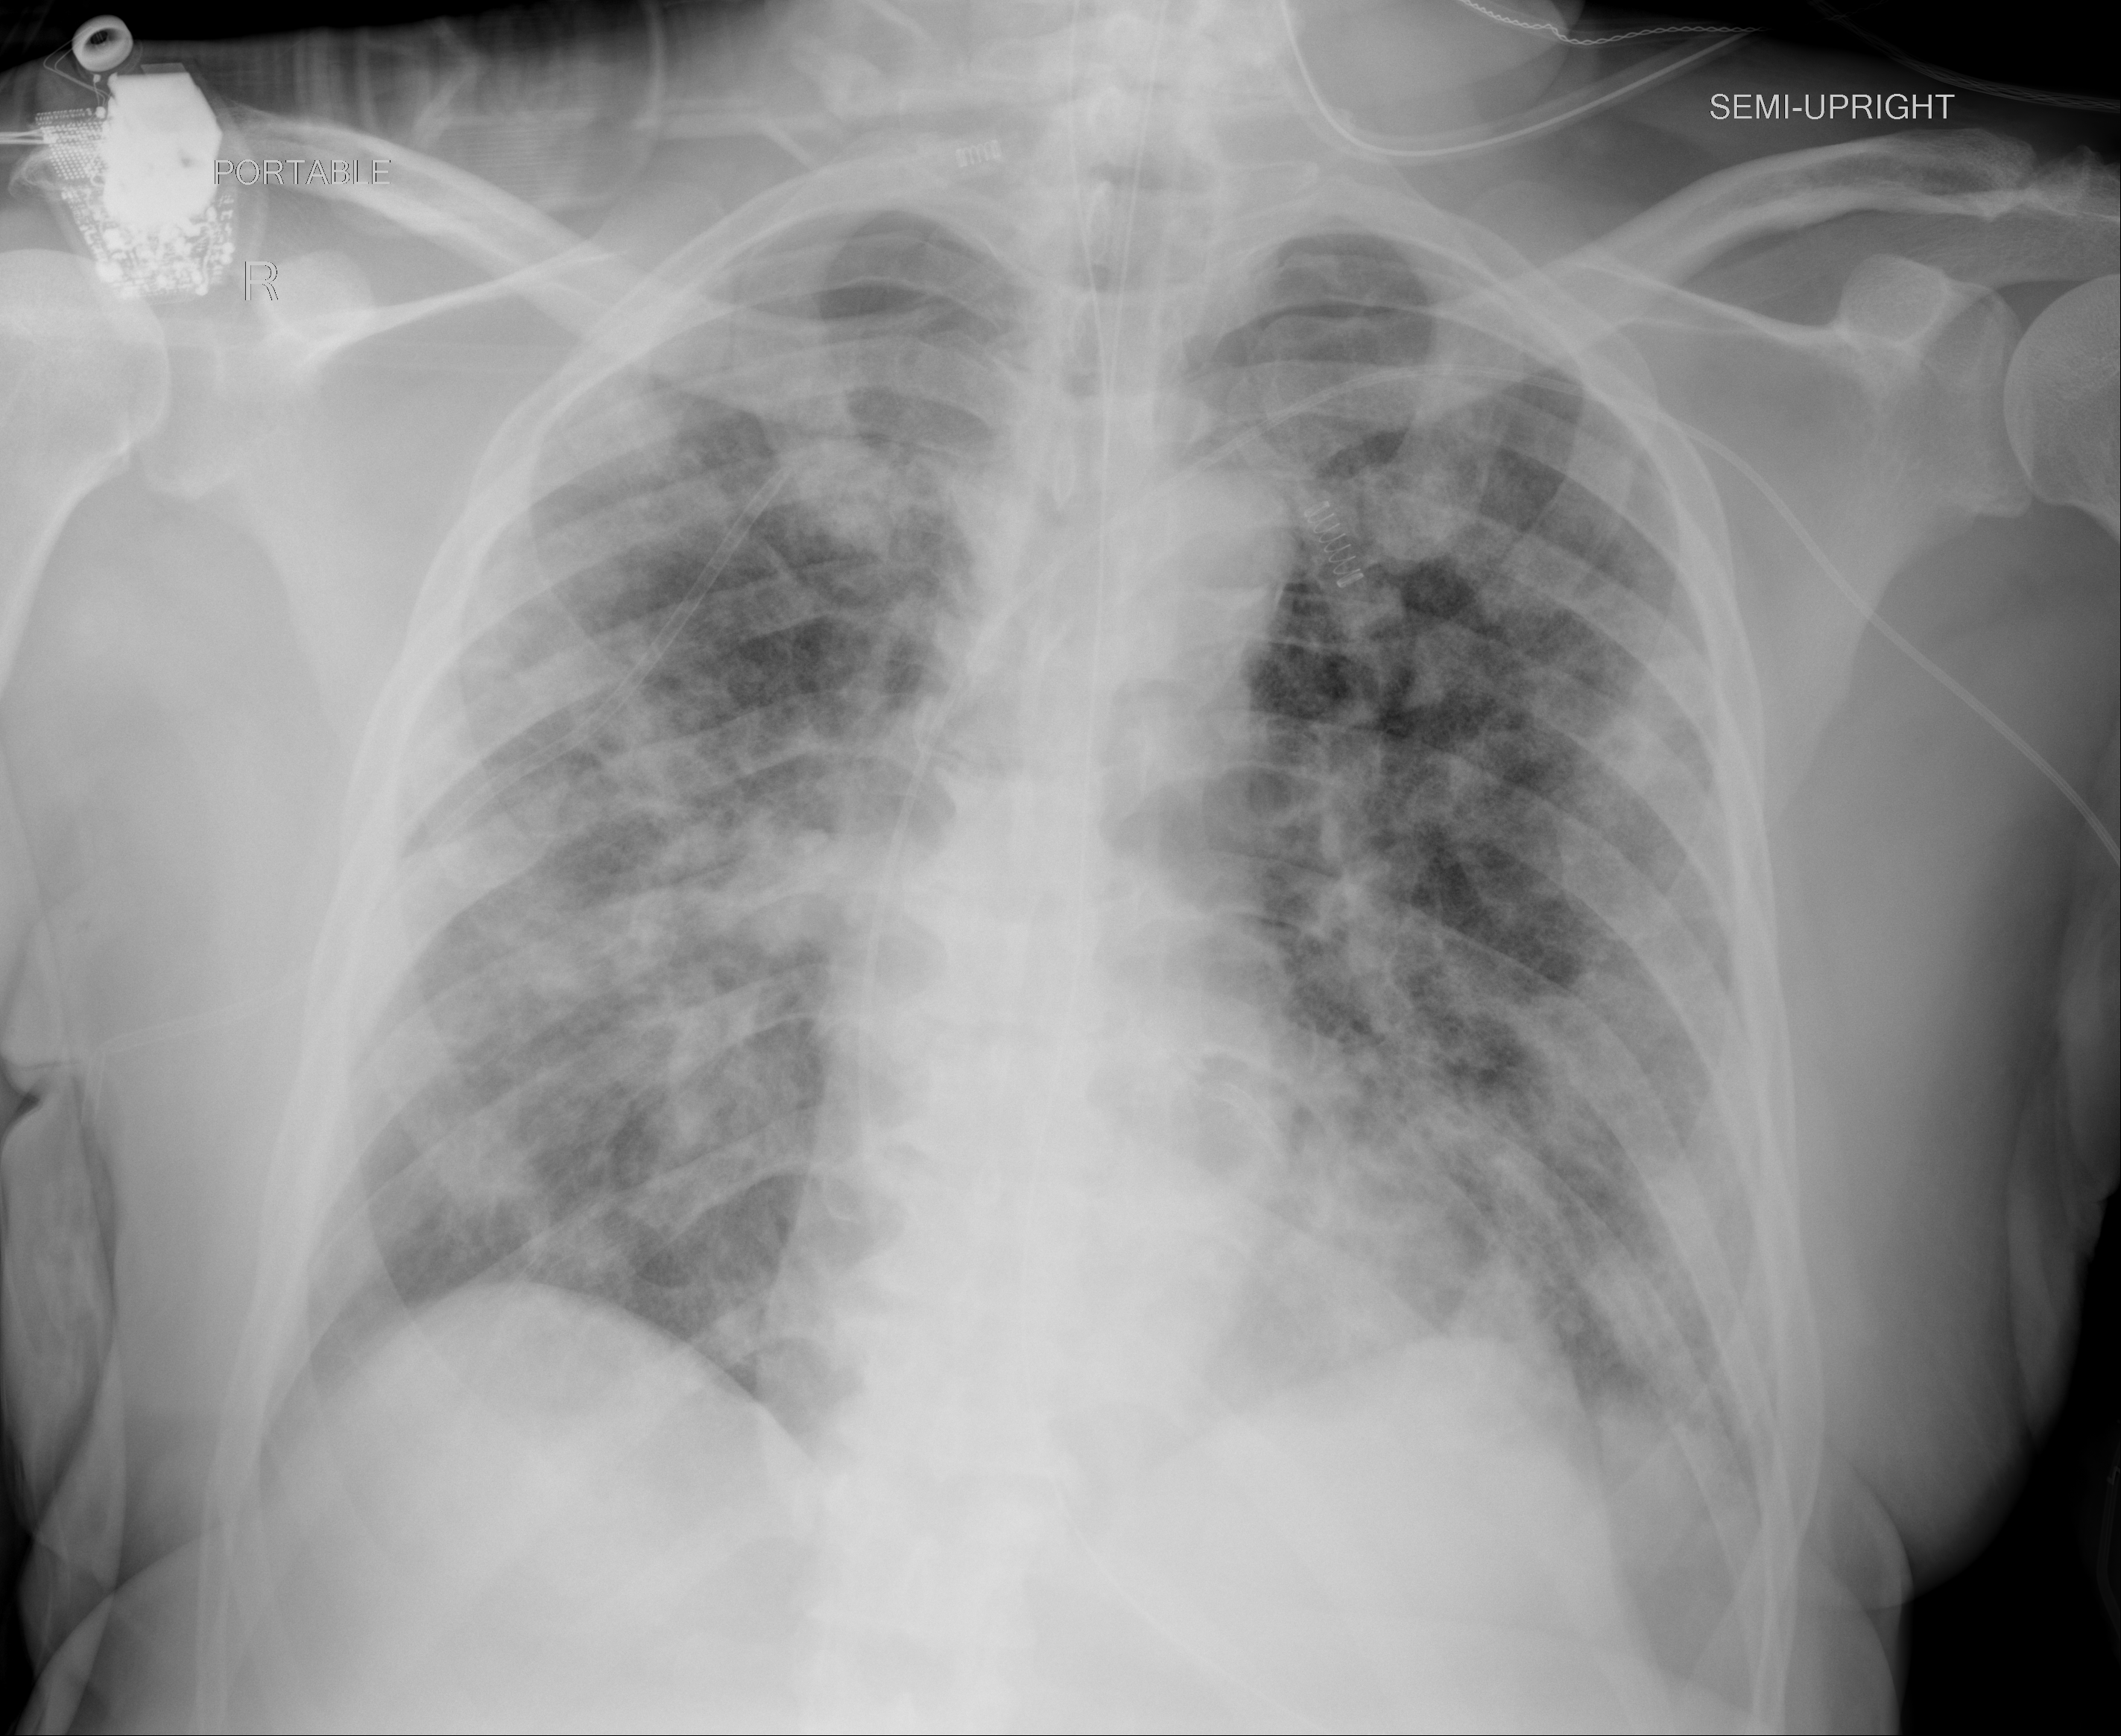
Portable chest radiograph, AP projection. Male patient, age 64 years; imaged 9 days after the COVID-19 diagnosis.
Key findings recorded by the radiologist: Stable patchy opacities throughout both lungs.